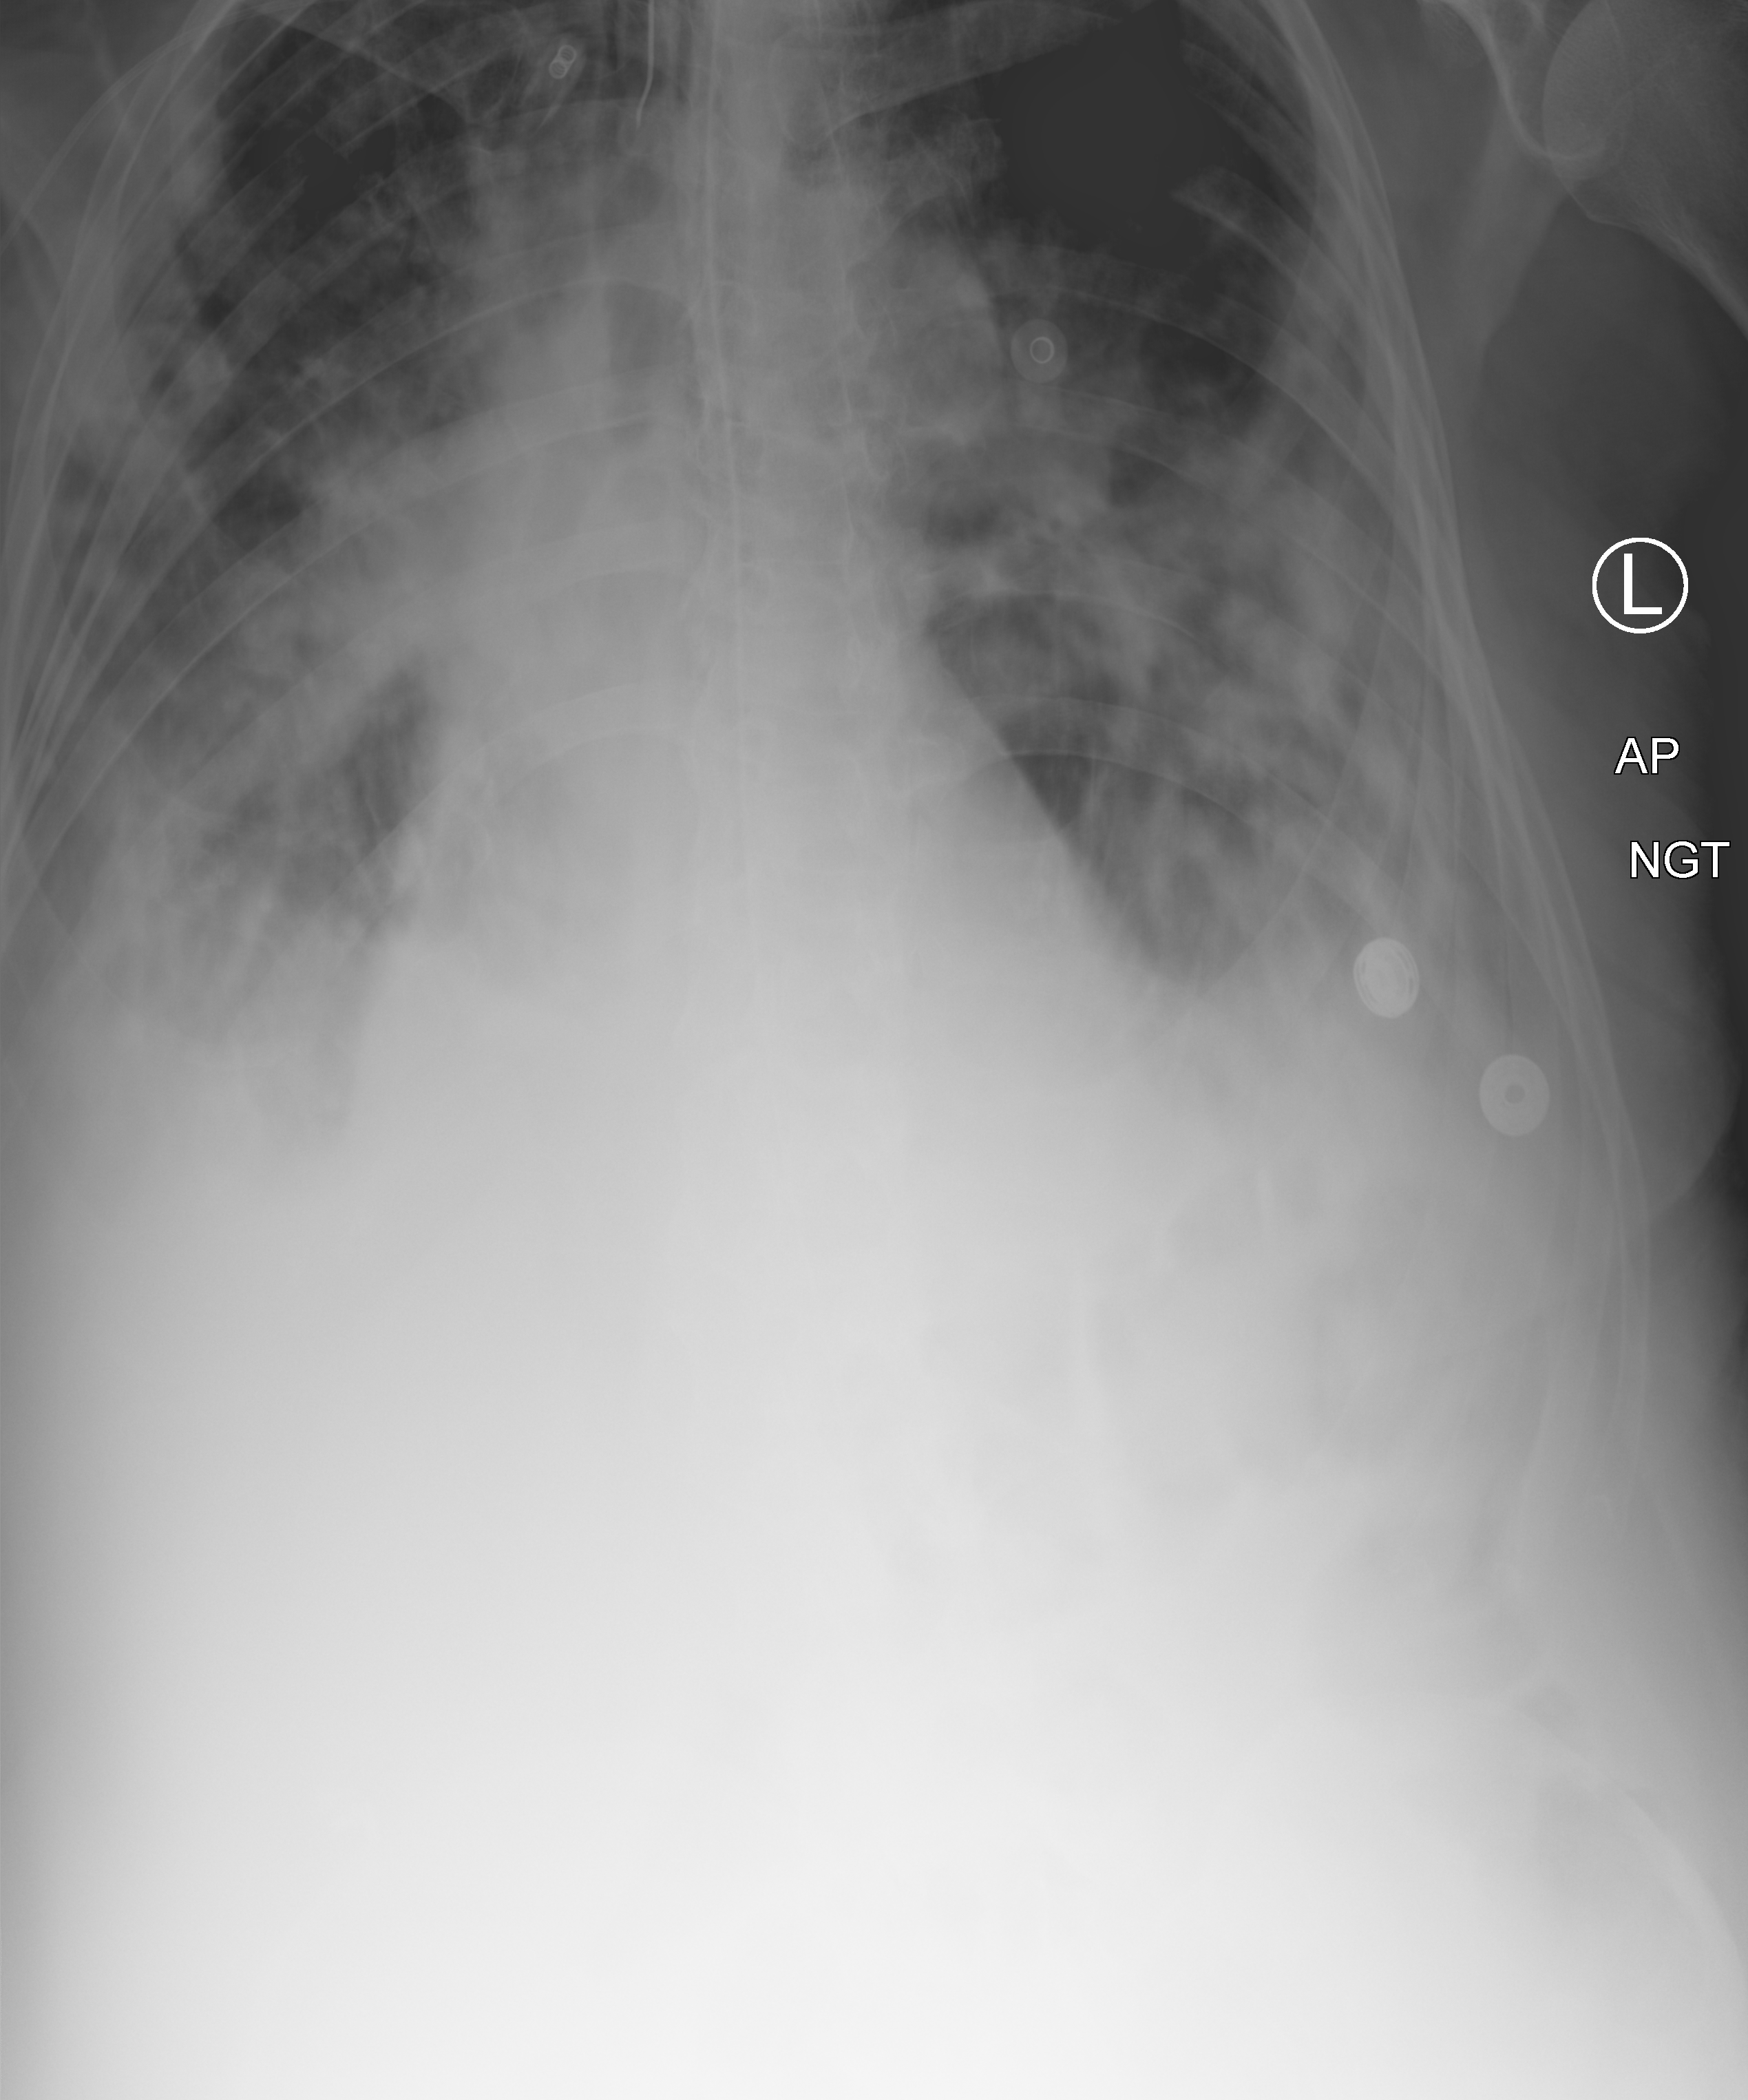
Abdomen X-ray (portable); anteroposterior (AP) projection. Patient hospitalised with COVID-19; male, aged 75–90 years.
From the hospital-stay record, not from the radiograph (when in the stay this image was taken is not recorded):
- mechanically ventilated during this hospital stay: yes
- length of hospital stay: 70 days